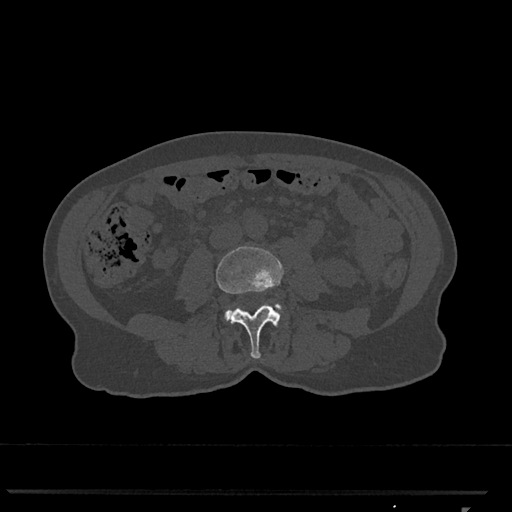
CT including the spine, one axial slice; position 255 of 793 along the scan axis; reconstruction kernel Br40s/3; 120 kVp; bone window (W 1800 / L 400 HU); 0.5 mm slice thickness; 512 × 512 image matrix, field of view 380 × 380 mm. Female patient, age 62 years. From the clinical record (not read from this slice): primary cancer: renal.
Structures marked on this image (semi-automatically segmented with operator editing):
- L3 vertebra: box from (x=216, y=246) to (x=283, y=359) px
- L4 vertebra: (x=224, y=304)–(x=283, y=321)